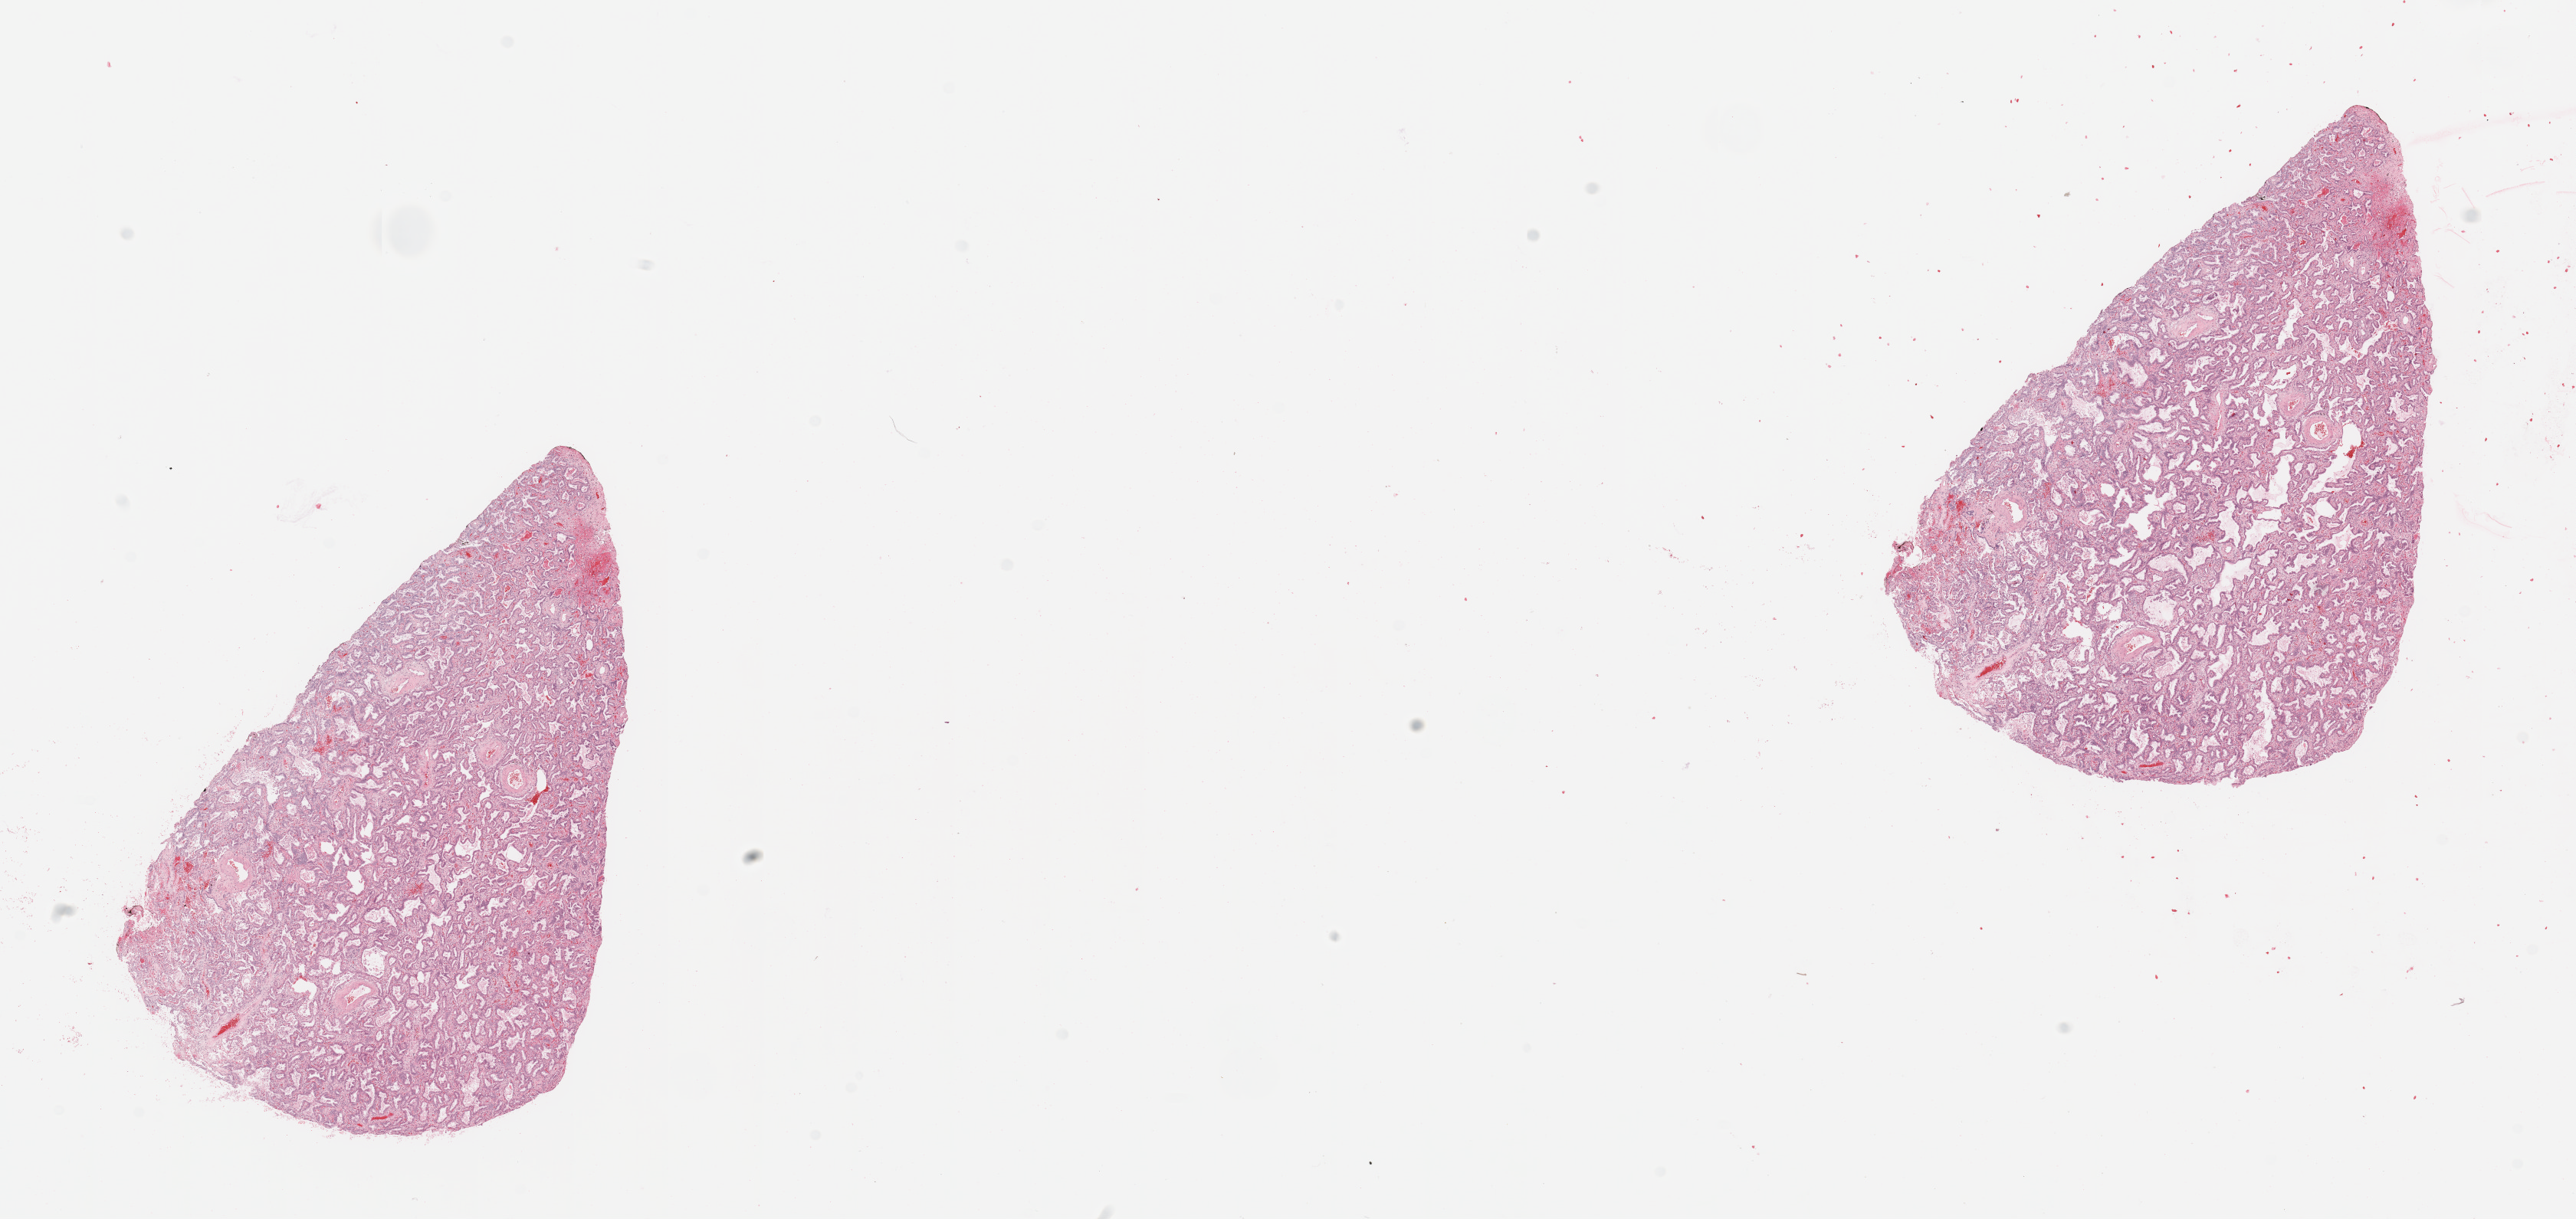
Whole-slide histology image, H&E-stained — whole scanned area (about 26.6 x 12.6 mm, slide scanned at 20x) shown as a low-resolution overview. Lung, tumour tissue. 78-year-old male patient. Histologic grade: G1 (well differentiated).
Histologic diagnosis: Adenocarcinoma, NOS. AJCC pathologic stage: IA. Primary tumour site (as recorded): right lower lobe.